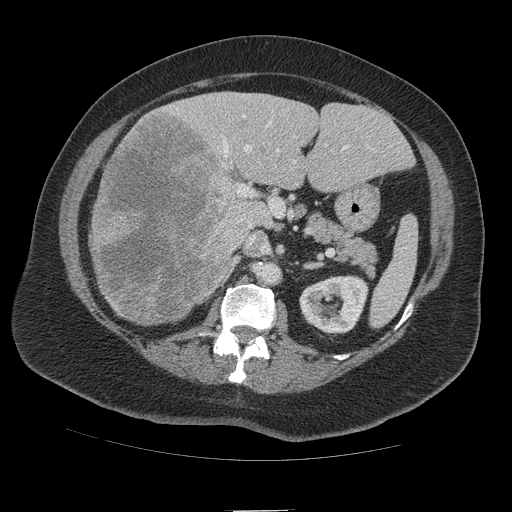
Contrast-enhanced abdominal CT (liver protocol), one axial slice; position 54 of 109 along the scan axis; reconstruction kernel STANDARD; soft-tissue window (W 400 / L 40 HU); 2.5 mm slice thickness; 512 × 512 image matrix, field of view 420 × 420 mm. From the clinical record (not read from this slice): diagnosis: hepatocellular carcinoma (patient treated with transarterial chemoembolisation; whether this scan precedes or follows treatment is not stated here); TNM stage (as recorded): Stage-IVB; Child-Pugh class: A; tumour differentiation: poorly differentiated.
Structures marked on this image (semi-automatically segmented with operator editing):
- liver parenchyma outside the tumour (the mass and vessels are separate outlines, so this box may not span the whole liver): box from (x=90, y=92) to (x=412, y=324) px
- mass: (x=91, y=109)–(x=249, y=324)
- liver vessels: (x=177, y=109)–(x=373, y=251)